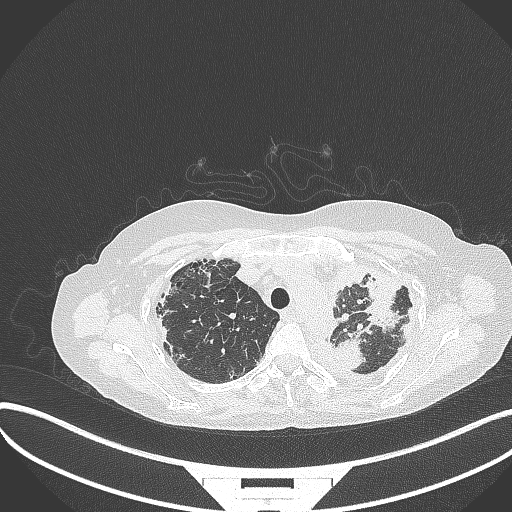
Chest CT, one axial slice; slice 269 of 373 in the series (ordered by position); reconstruction kernel B70f; 120 kVp; lung window (W 1500 / L -600 HU); 1 mm slice thickness; 512 × 512 image matrix. Patient: female, 56 years. From the clinical record (not read from this slice): clinical TNM (as recorded): T1 N0 M0.
Annotated regions visible in this slice (bounding box drawn by a radiologist):
- lung tumour (recorded histology: adenocarcinoma): bounding box (x1, y1, x2, y2) in pixels: (329, 333, 370, 377)
- lung tumour (recorded histology: adenocarcinoma): (356, 269, 408, 338)